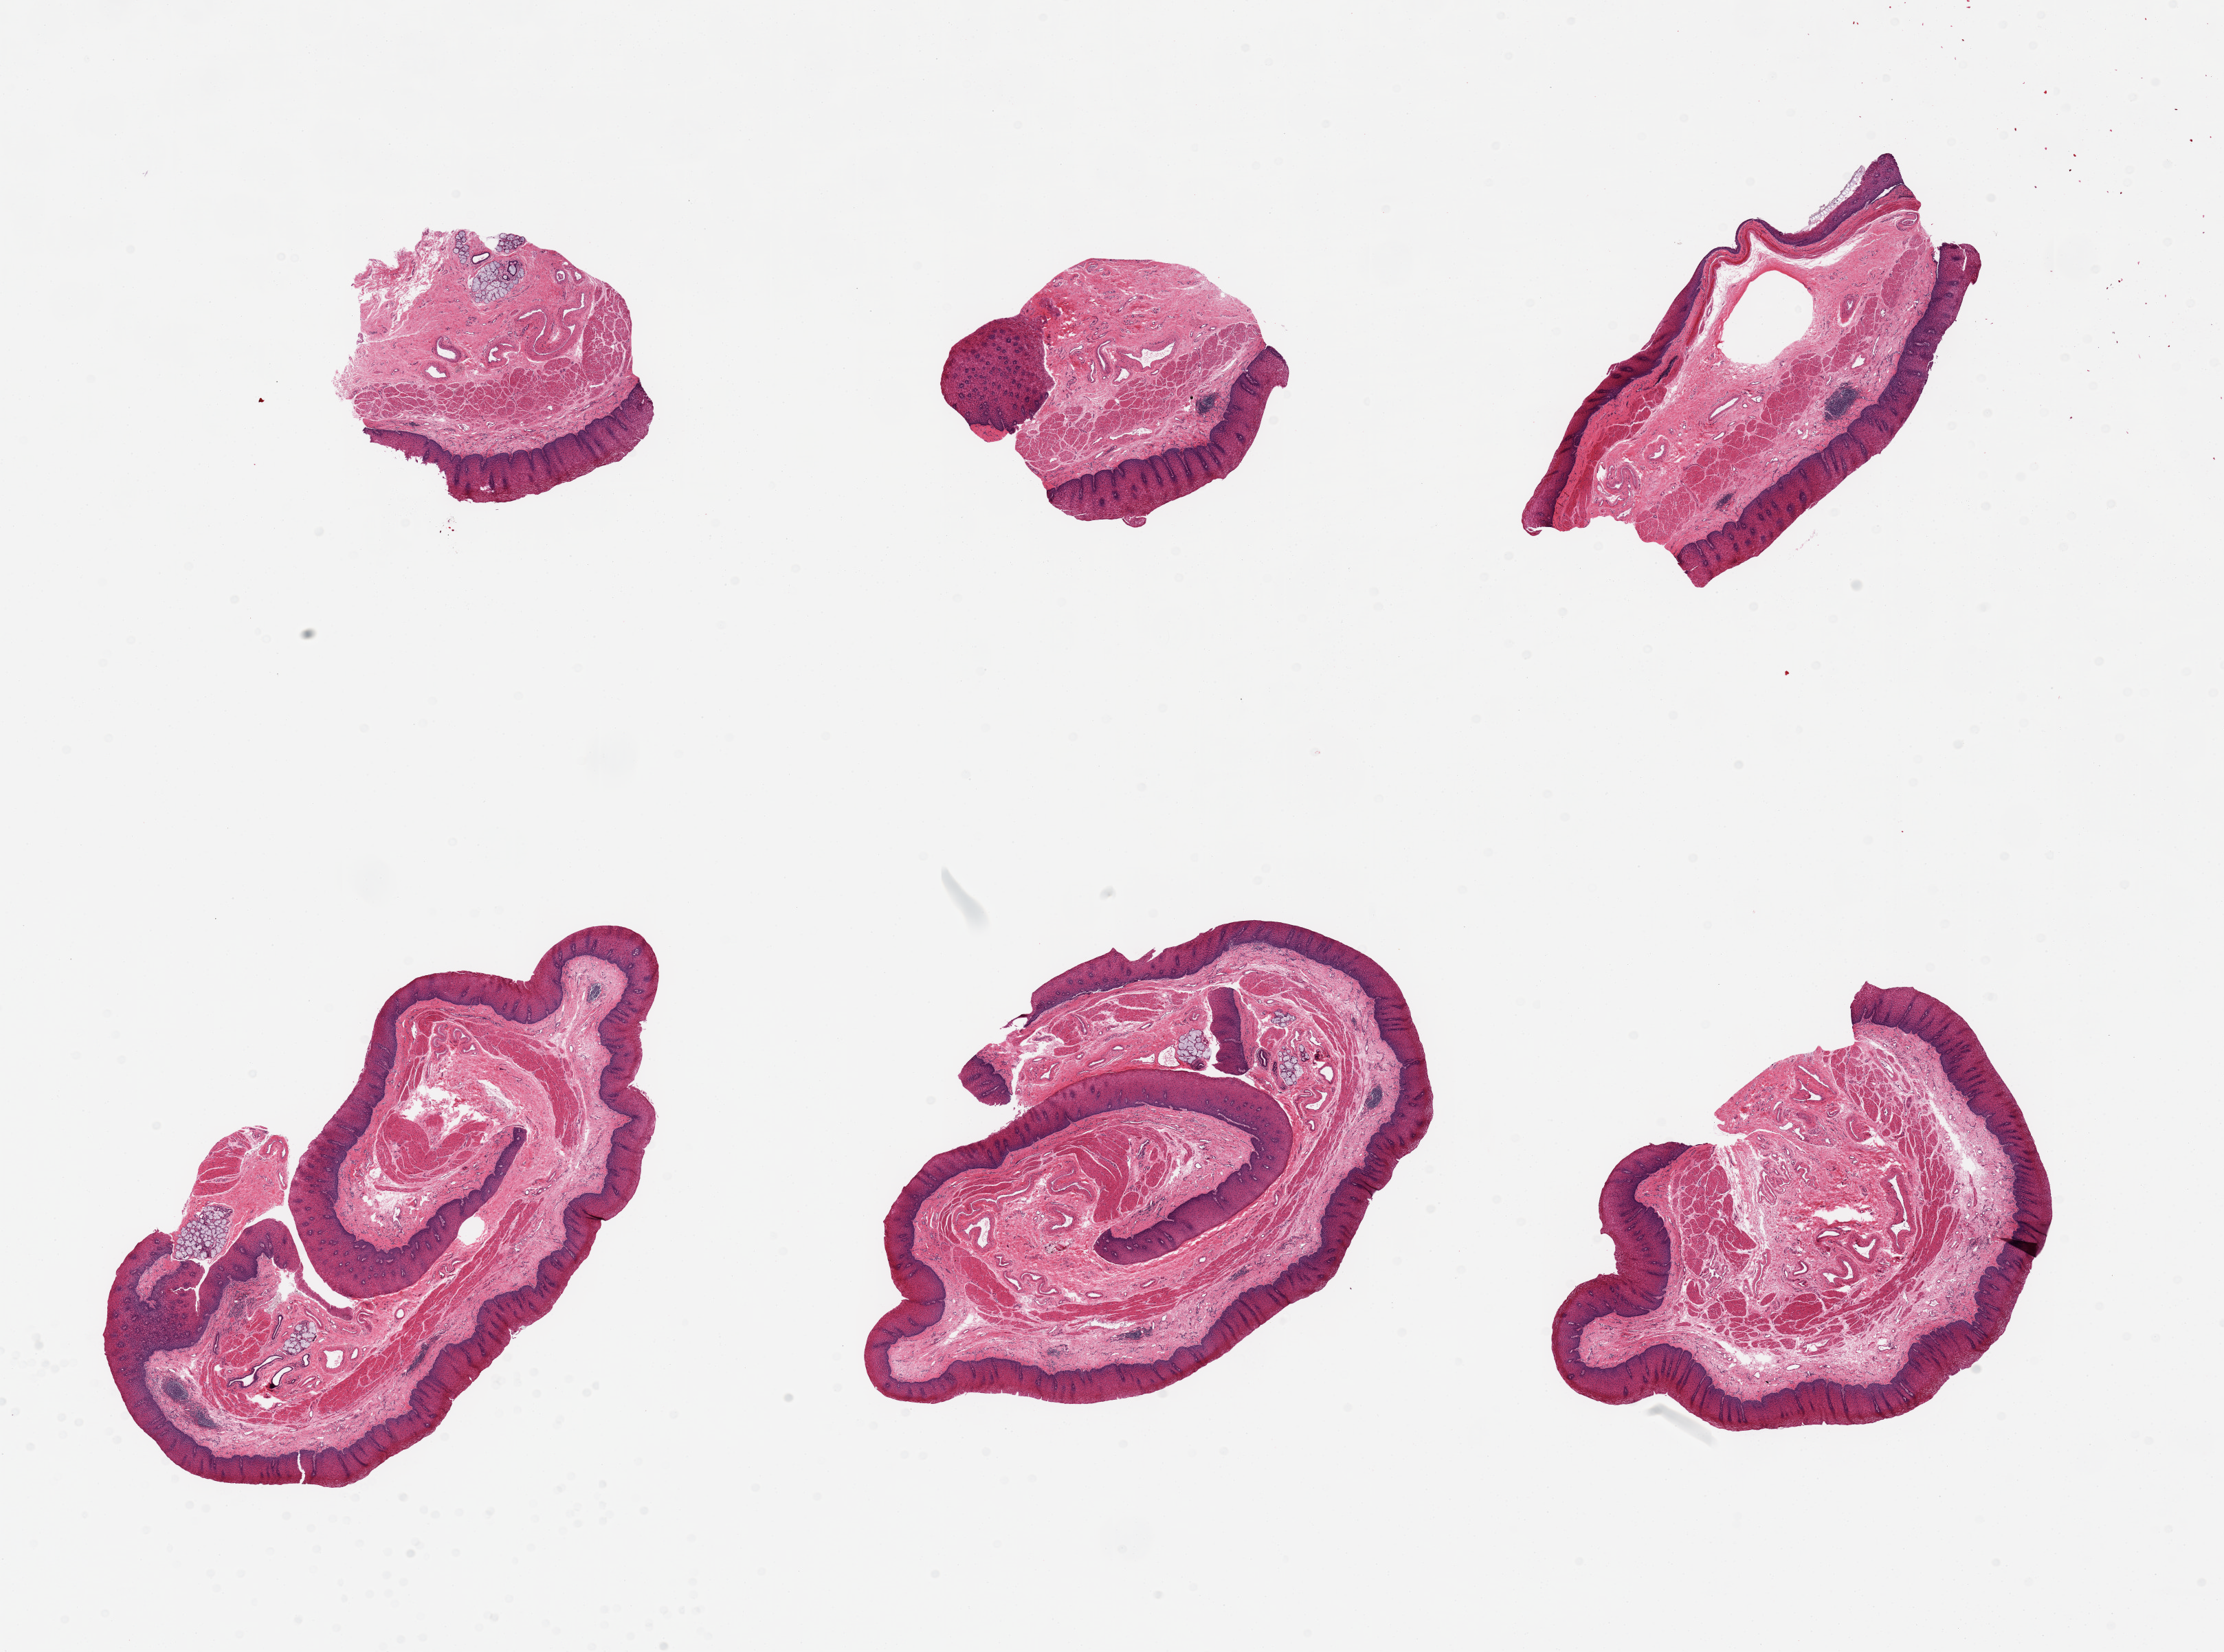
Whole-slide image, hematoxylin and eosin (H&E) stain, a low-resolution overview of the entire scanned area, about 25.6 x 19.0 mm, PAXgene-fixed, paraffin-embedded tissue, section of esophageal mucous membrane (target tissue), donor tissue sample.
Reviewer comment on this tissue sample: 6 pieces.